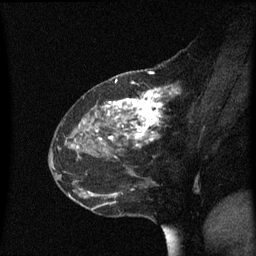
Breast MRI (dynamic contrast-enhanced), one sagittal slice; slice 24 of 60 in the series (ordered by position); dynamic contrast-enhanced series, image 2 of 3 at this slice position (ordered by acquisition); 1.5 T; TE 4.2 ms, TR 8.4 ms; 2 mm slice thickness; 256 × 256 image matrix. Female patient, age 48 years. From the clinical record (not read from this slice): setting: breast cancer imaged before/during neoadjuvant chemotherapy; receptor status: HR-positive, HER2-negative.
Structures marked on this image (semi-automatically segmented with operator editing):
- analysis volume of interest (the breast-tissue region the enhancement analysis was run in; not a lesion): bounding box <80,78,195,221> (left, top, right, bottom; pixels)
- tumour enhancement mask (voxels above the 70 % enhancement threshold inside the analysis volume of interest): <100,81,179,147>